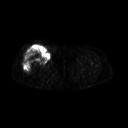
FDG PET of an extremity soft-tissue mass (from a PET/CT study), one axial slice. Slice 245 of 311 in the series (ordered by position). 3.27 mm slice thickness. 128 × 128 image matrix, field of view 500 × 500 mm. Female patient, age 57 years. From the clinical record (not read from this slice): histological type: pleiomorphic undifferentiated sarcoma; grade: high; site of the primary tumour: right quadricep.
Structures marked on this image (expert contour drawn on MRI and transferred to this co-registered scan by the dataset authors):
- tumour plus oedema (research contour): bounding box [x1, y1, x2, y2] px = [23, 46, 49, 71]
- tumour (research contour): [23, 46, 49, 71]